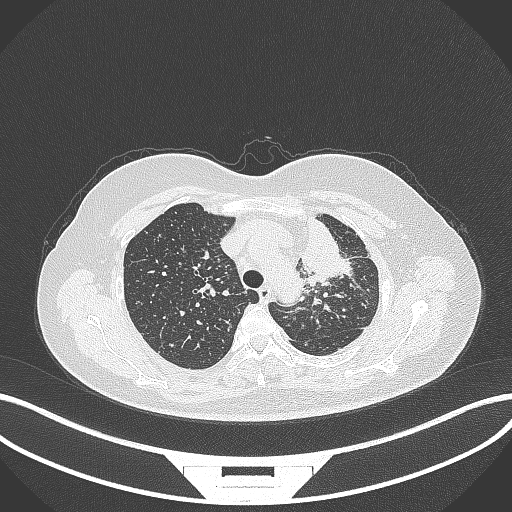
Chest CT, one axial slice. Slice 257 of 348 in the series (ordered by position). 120 kVp. Lung window (W 1500 / L -600 HU). 1 mm slice thickness. 512 × 512 image matrix, field of view 400 × 400 mm. Female patient, age 49 years. From the clinical record (not read from this slice): clinical TNM (as recorded): T1c N0 M1.
Annotated regions visible in this slice (bounding box drawn by a radiologist):
- lung tumour (recorded histology: adenocarcinoma): bounding box <292,221,355,283> (left, top, right, bottom; pixels)